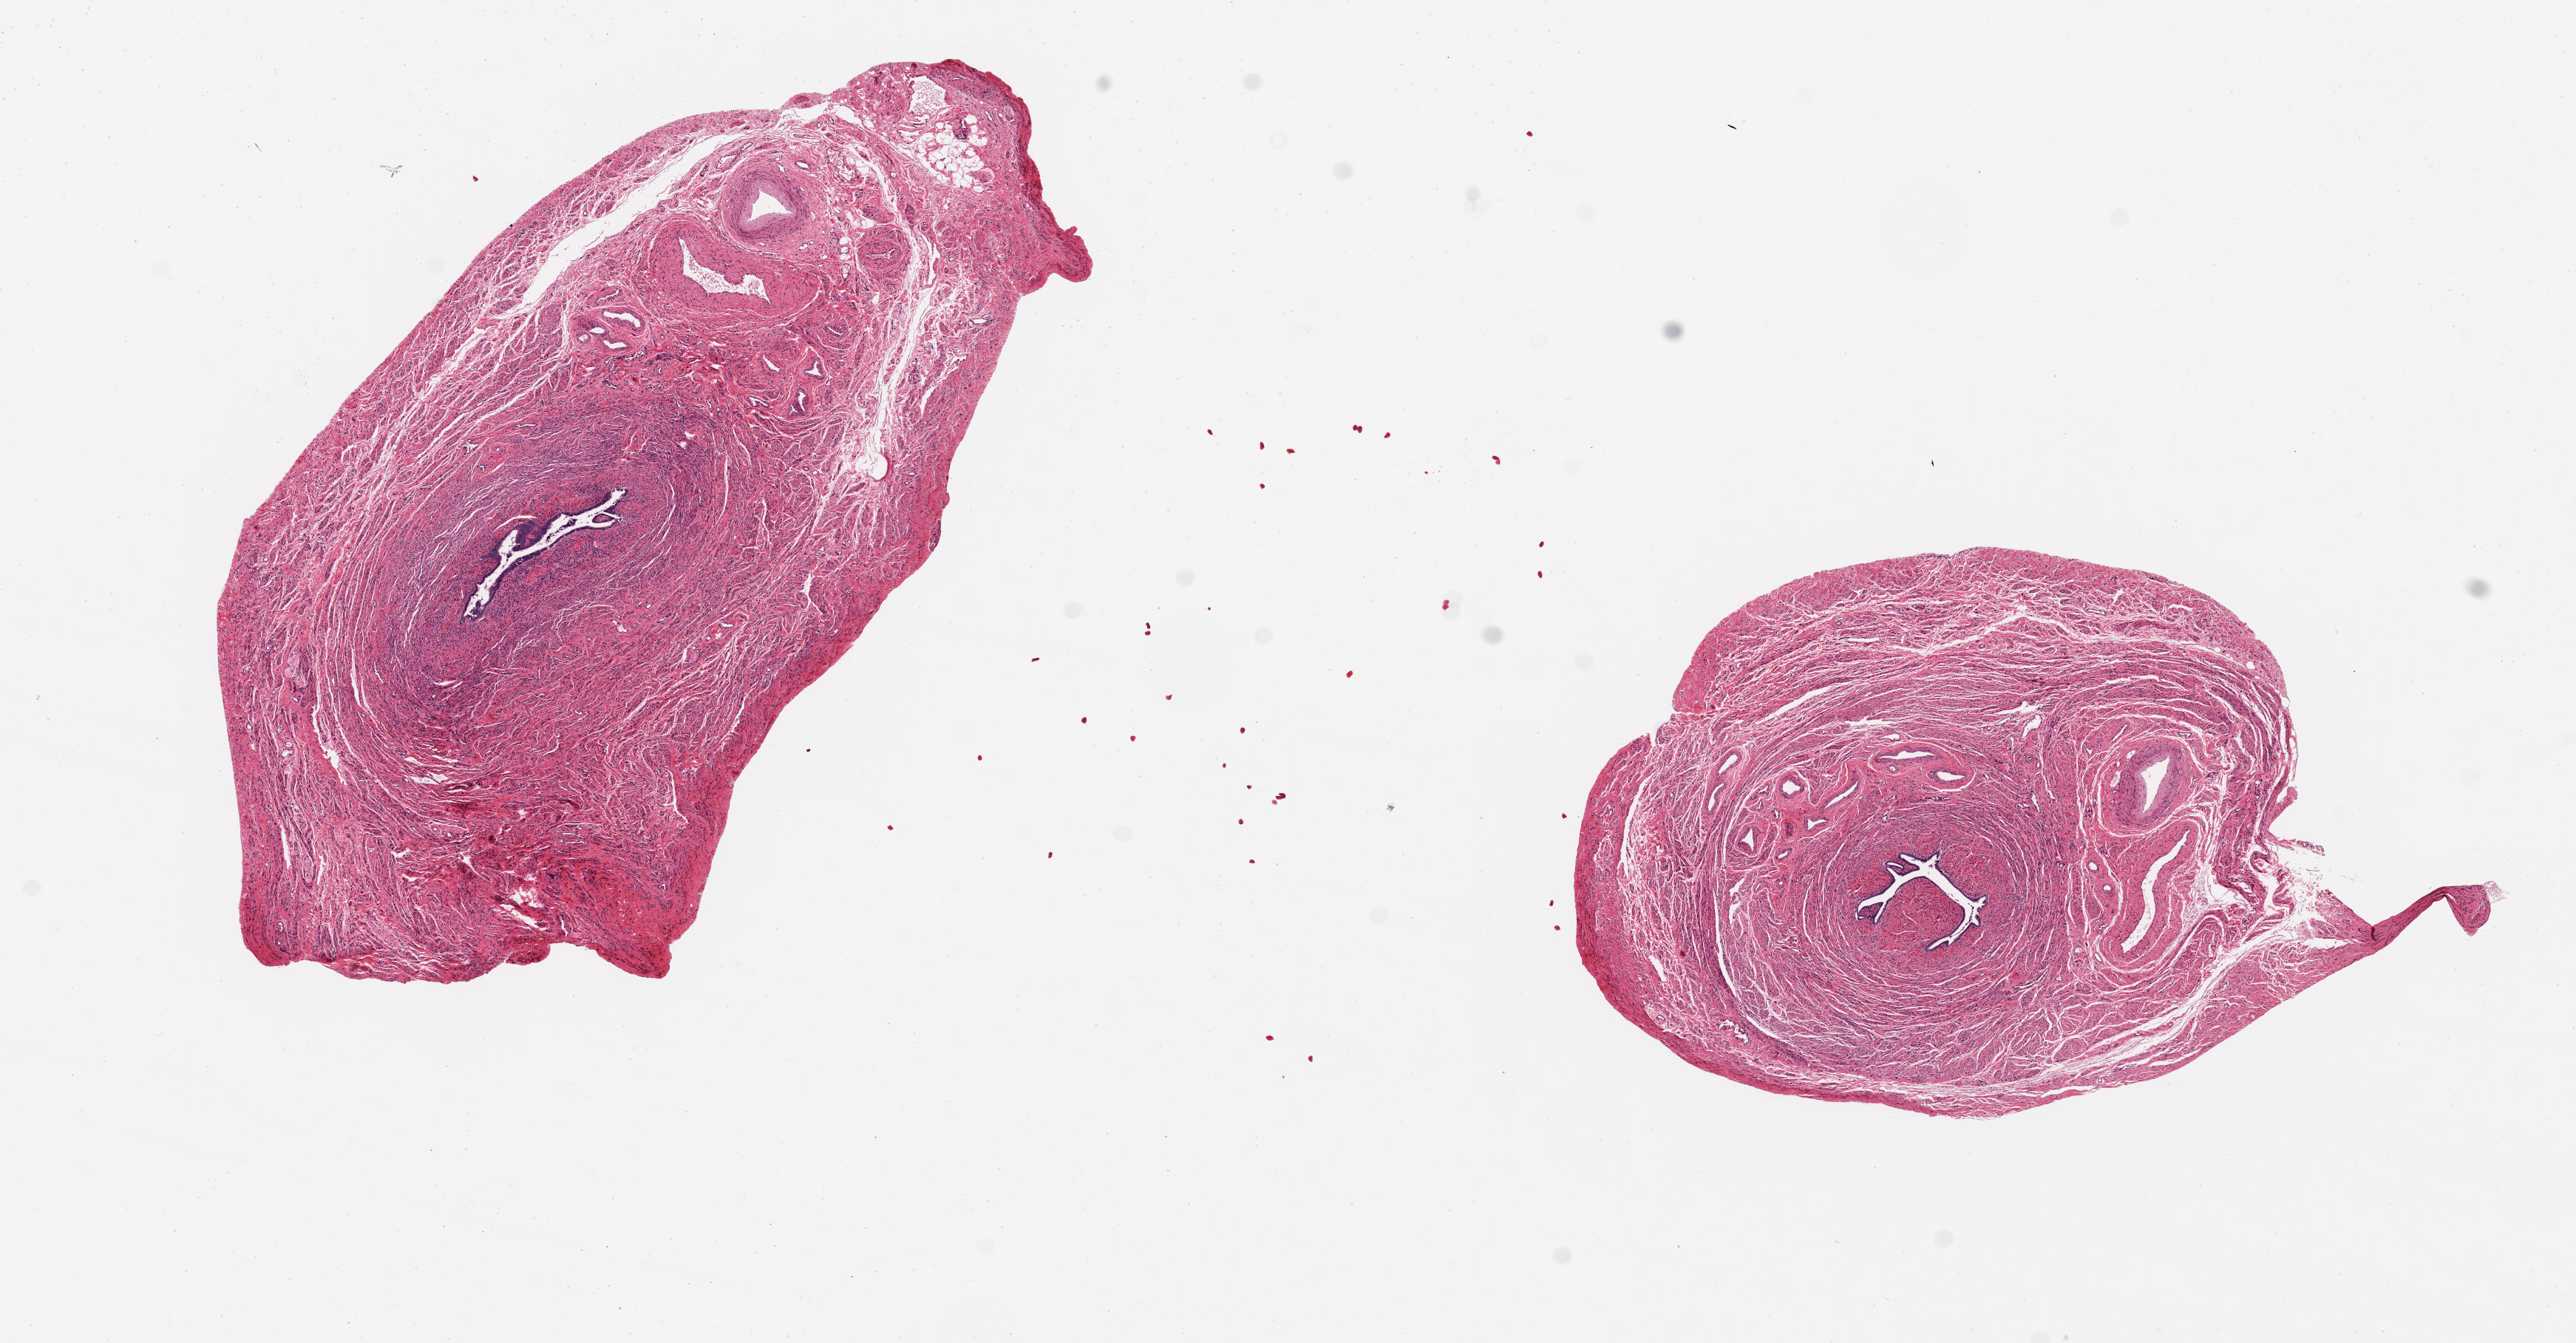
Digitized haematoxylin and eosin-stained section, brightfield — shown as a low-resolution overview of the whole scanned area (about 13.8 x 7.2 mm, from a 20x scan); PAXgene-fixed paraffin-embedded (PFPE) section; target tissue: fallopian tube; tissue donor sample. Donor sex: female.
Pathologist's review note for this sample: 2 pieces ~6x3 & 3x2.8; needs re-labeling.